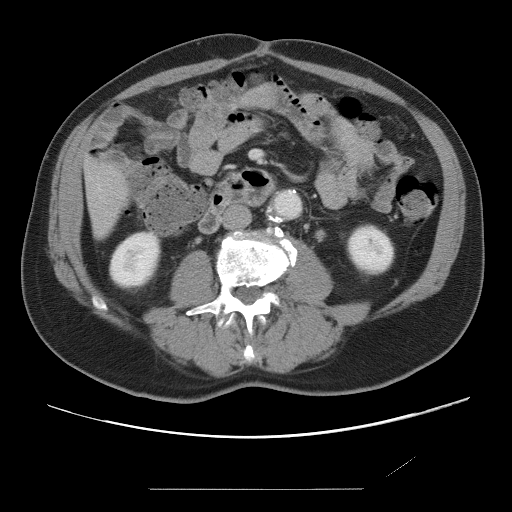
Contrast-enhanced abdominal CT, one axial slice; position 12 of 87 along the scan axis; 120 kVp; intravenous contrast given; soft-tissue window (W 400 / L 40 HU); 5 mm slice thickness; 512 × 512 image matrix, field of view 406 × 406 mm. Male patient, age 74 years. Case-level facts recorded for this patient, not image findings: diagnosis: colorectal cancer liver metastases, imaged before liver resection; multiple liver metastases: yes; largest metastasis: 1.1 cm; disease in both lobes: no.
Annotated regions visible in this slice (manually delineated by an expert):
- liver: bounding box [x1, y1, x2, y2] px = [85, 159, 124, 235]
- planned liver remnant (the part of the liver to remain after resection): [85, 159, 124, 235]